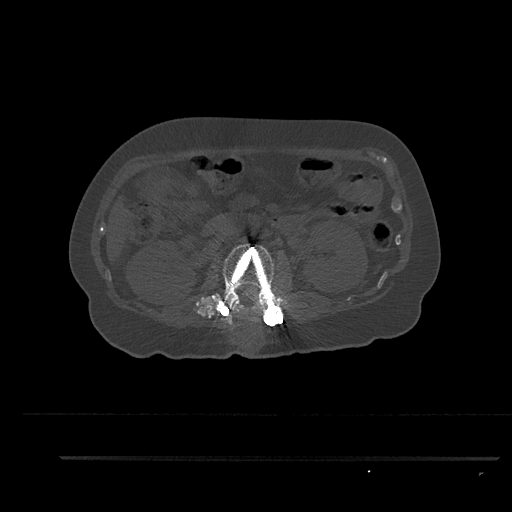
CT including the spine, one axial slice. Position 174 of 797 along the scan axis. Reconstruction kernel Br40s/3. Bone window (W 1800 / L 400 HU). 0.5 mm slice thickness. 512 × 512 image matrix, field of view 408 × 408 mm. Female patient, age 44 years. Case-level facts recorded for this patient, not image findings: primary cancer: renal; vertebrae with lytic lesions (as recorded): L1.
Annotated regions visible in this slice (semi-automatically segmented with operator editing):
- L2 vertebra: box from (x=213, y=243) to (x=276, y=320) px